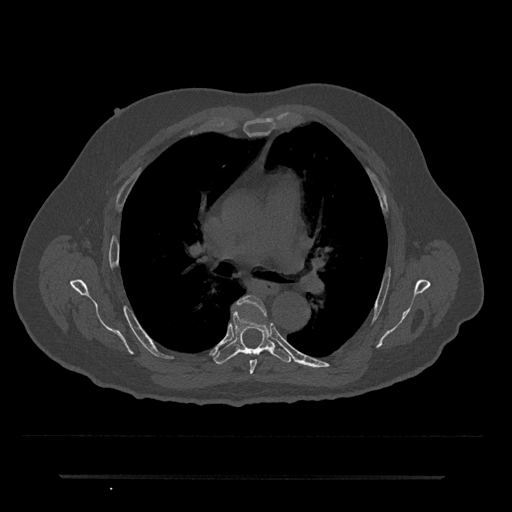
CT including the spine, one axial slice; slice 453 of 797 in the series (ordered by position); reconstruction kernel Br40s/3; 120 kVp; bone window (W 1800 / L 400 HU); 0.5 mm slice thickness; 512 × 512 image matrix, field of view 437 × 437 mm. Patient: male, 69 years. From the clinical record (not read from this slice): primary cancer: prostate.
Annotated regions visible in this slice (semi-automatic segmentation, software-assisted and operator-edited):
- T5 vertebra: box from (x=233, y=296) to (x=266, y=375) px
- T6 vertebra: (x=214, y=310)–(x=292, y=364)